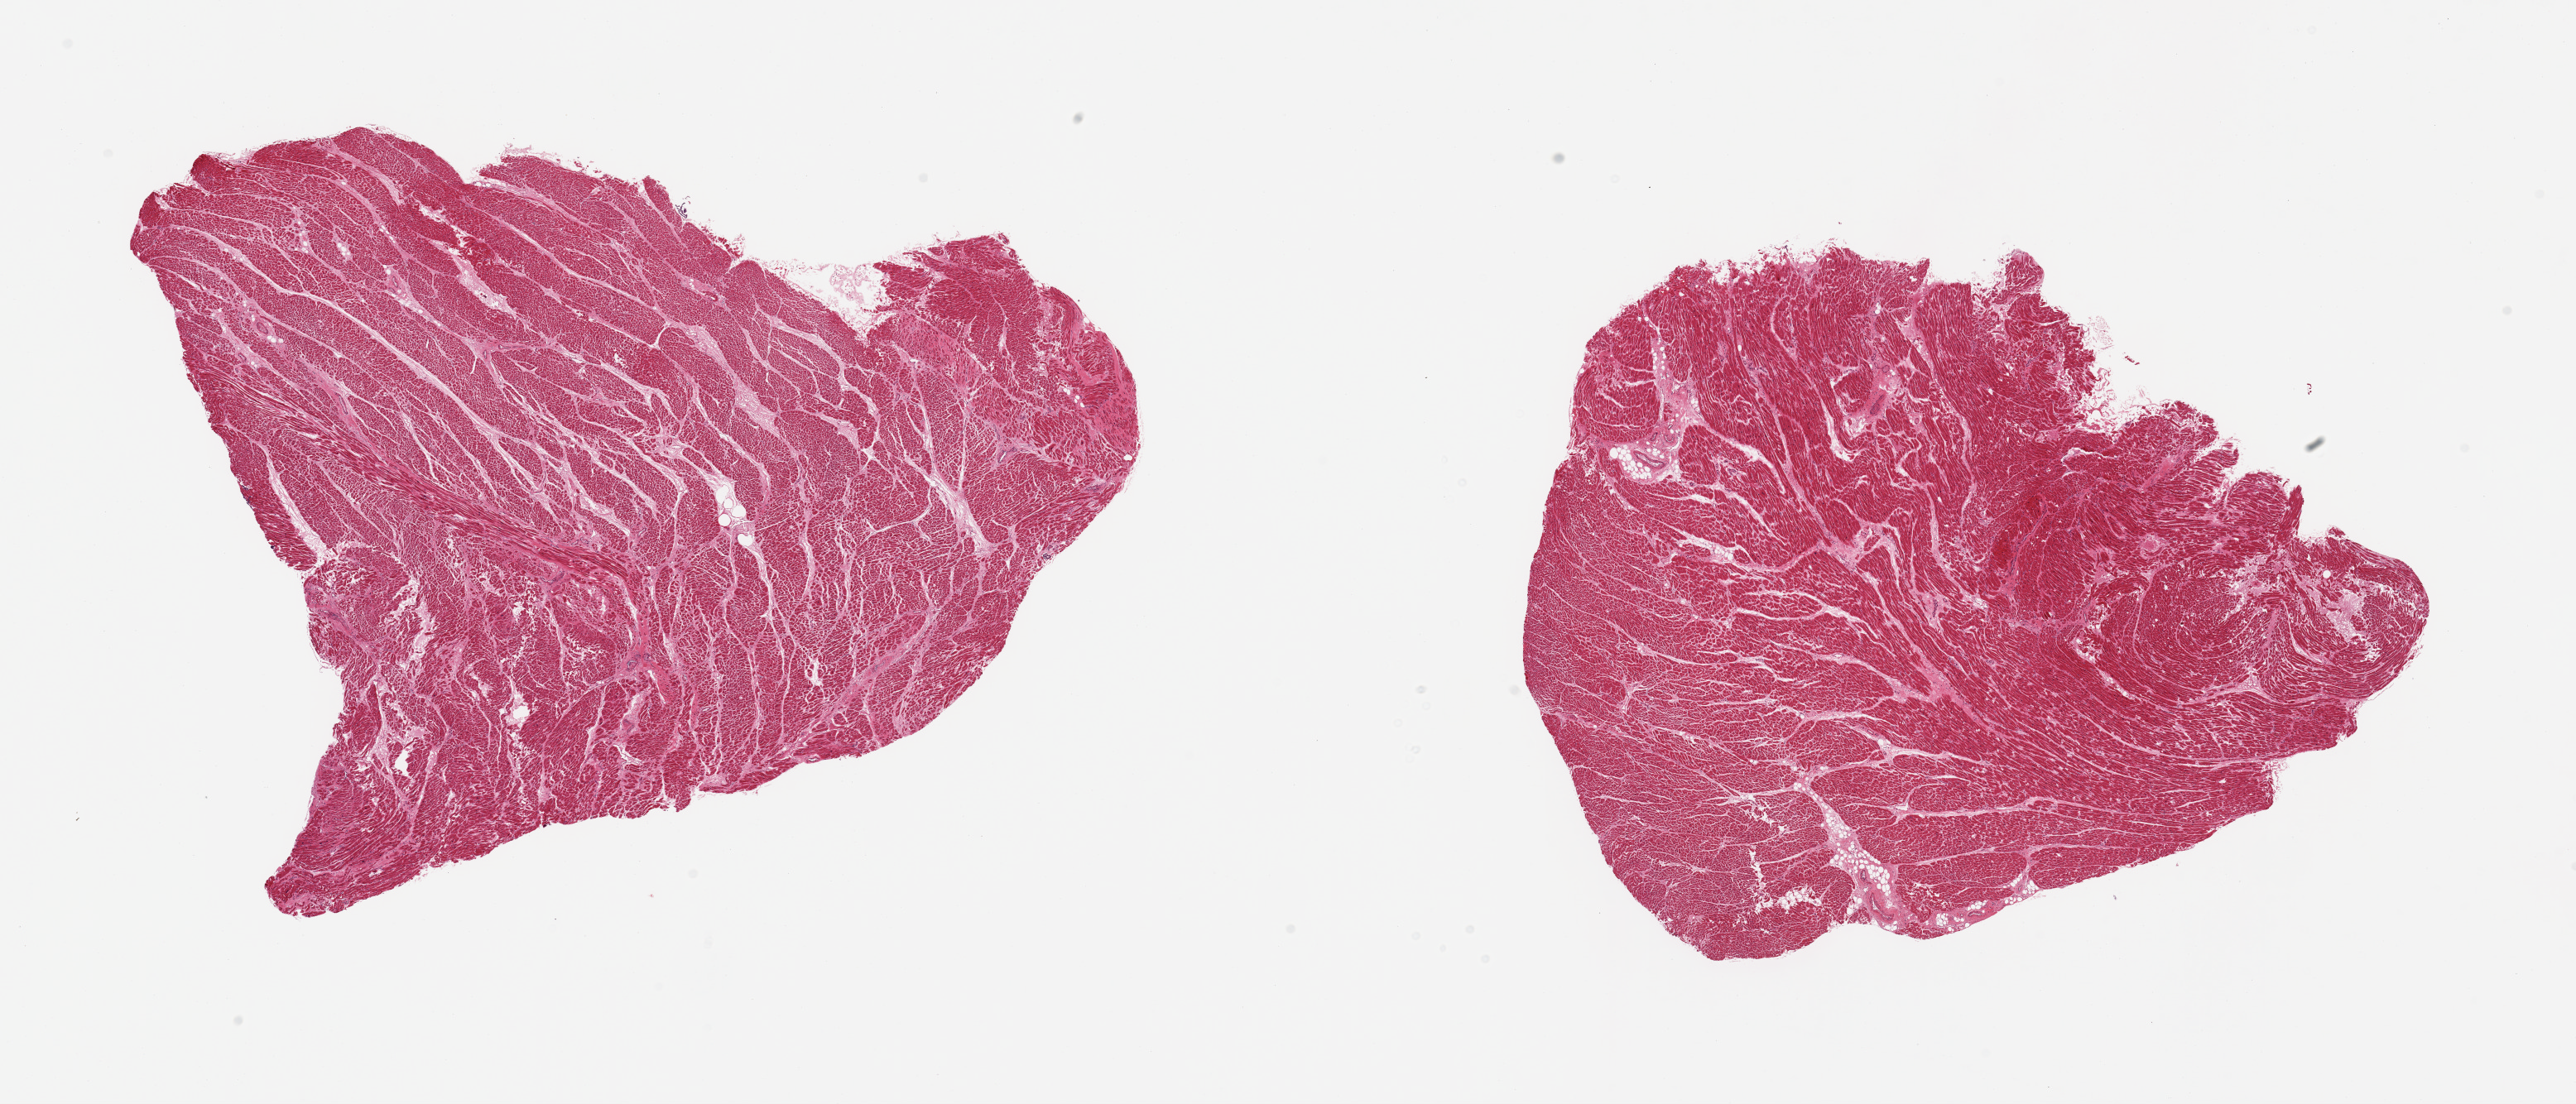
Whole-slide image, haematoxylin and eosin stain — a low-resolution overview of the entire scanned area, about 24.6 x 10.5 mm. PAXgene-fixed, paraffin-embedded tissue. Section of heart (target tissue). Donor tissue sample. Male donor.
Review note (as recorded): 2 pieces; mild interstitial fibrosis with patchy focal scarring.